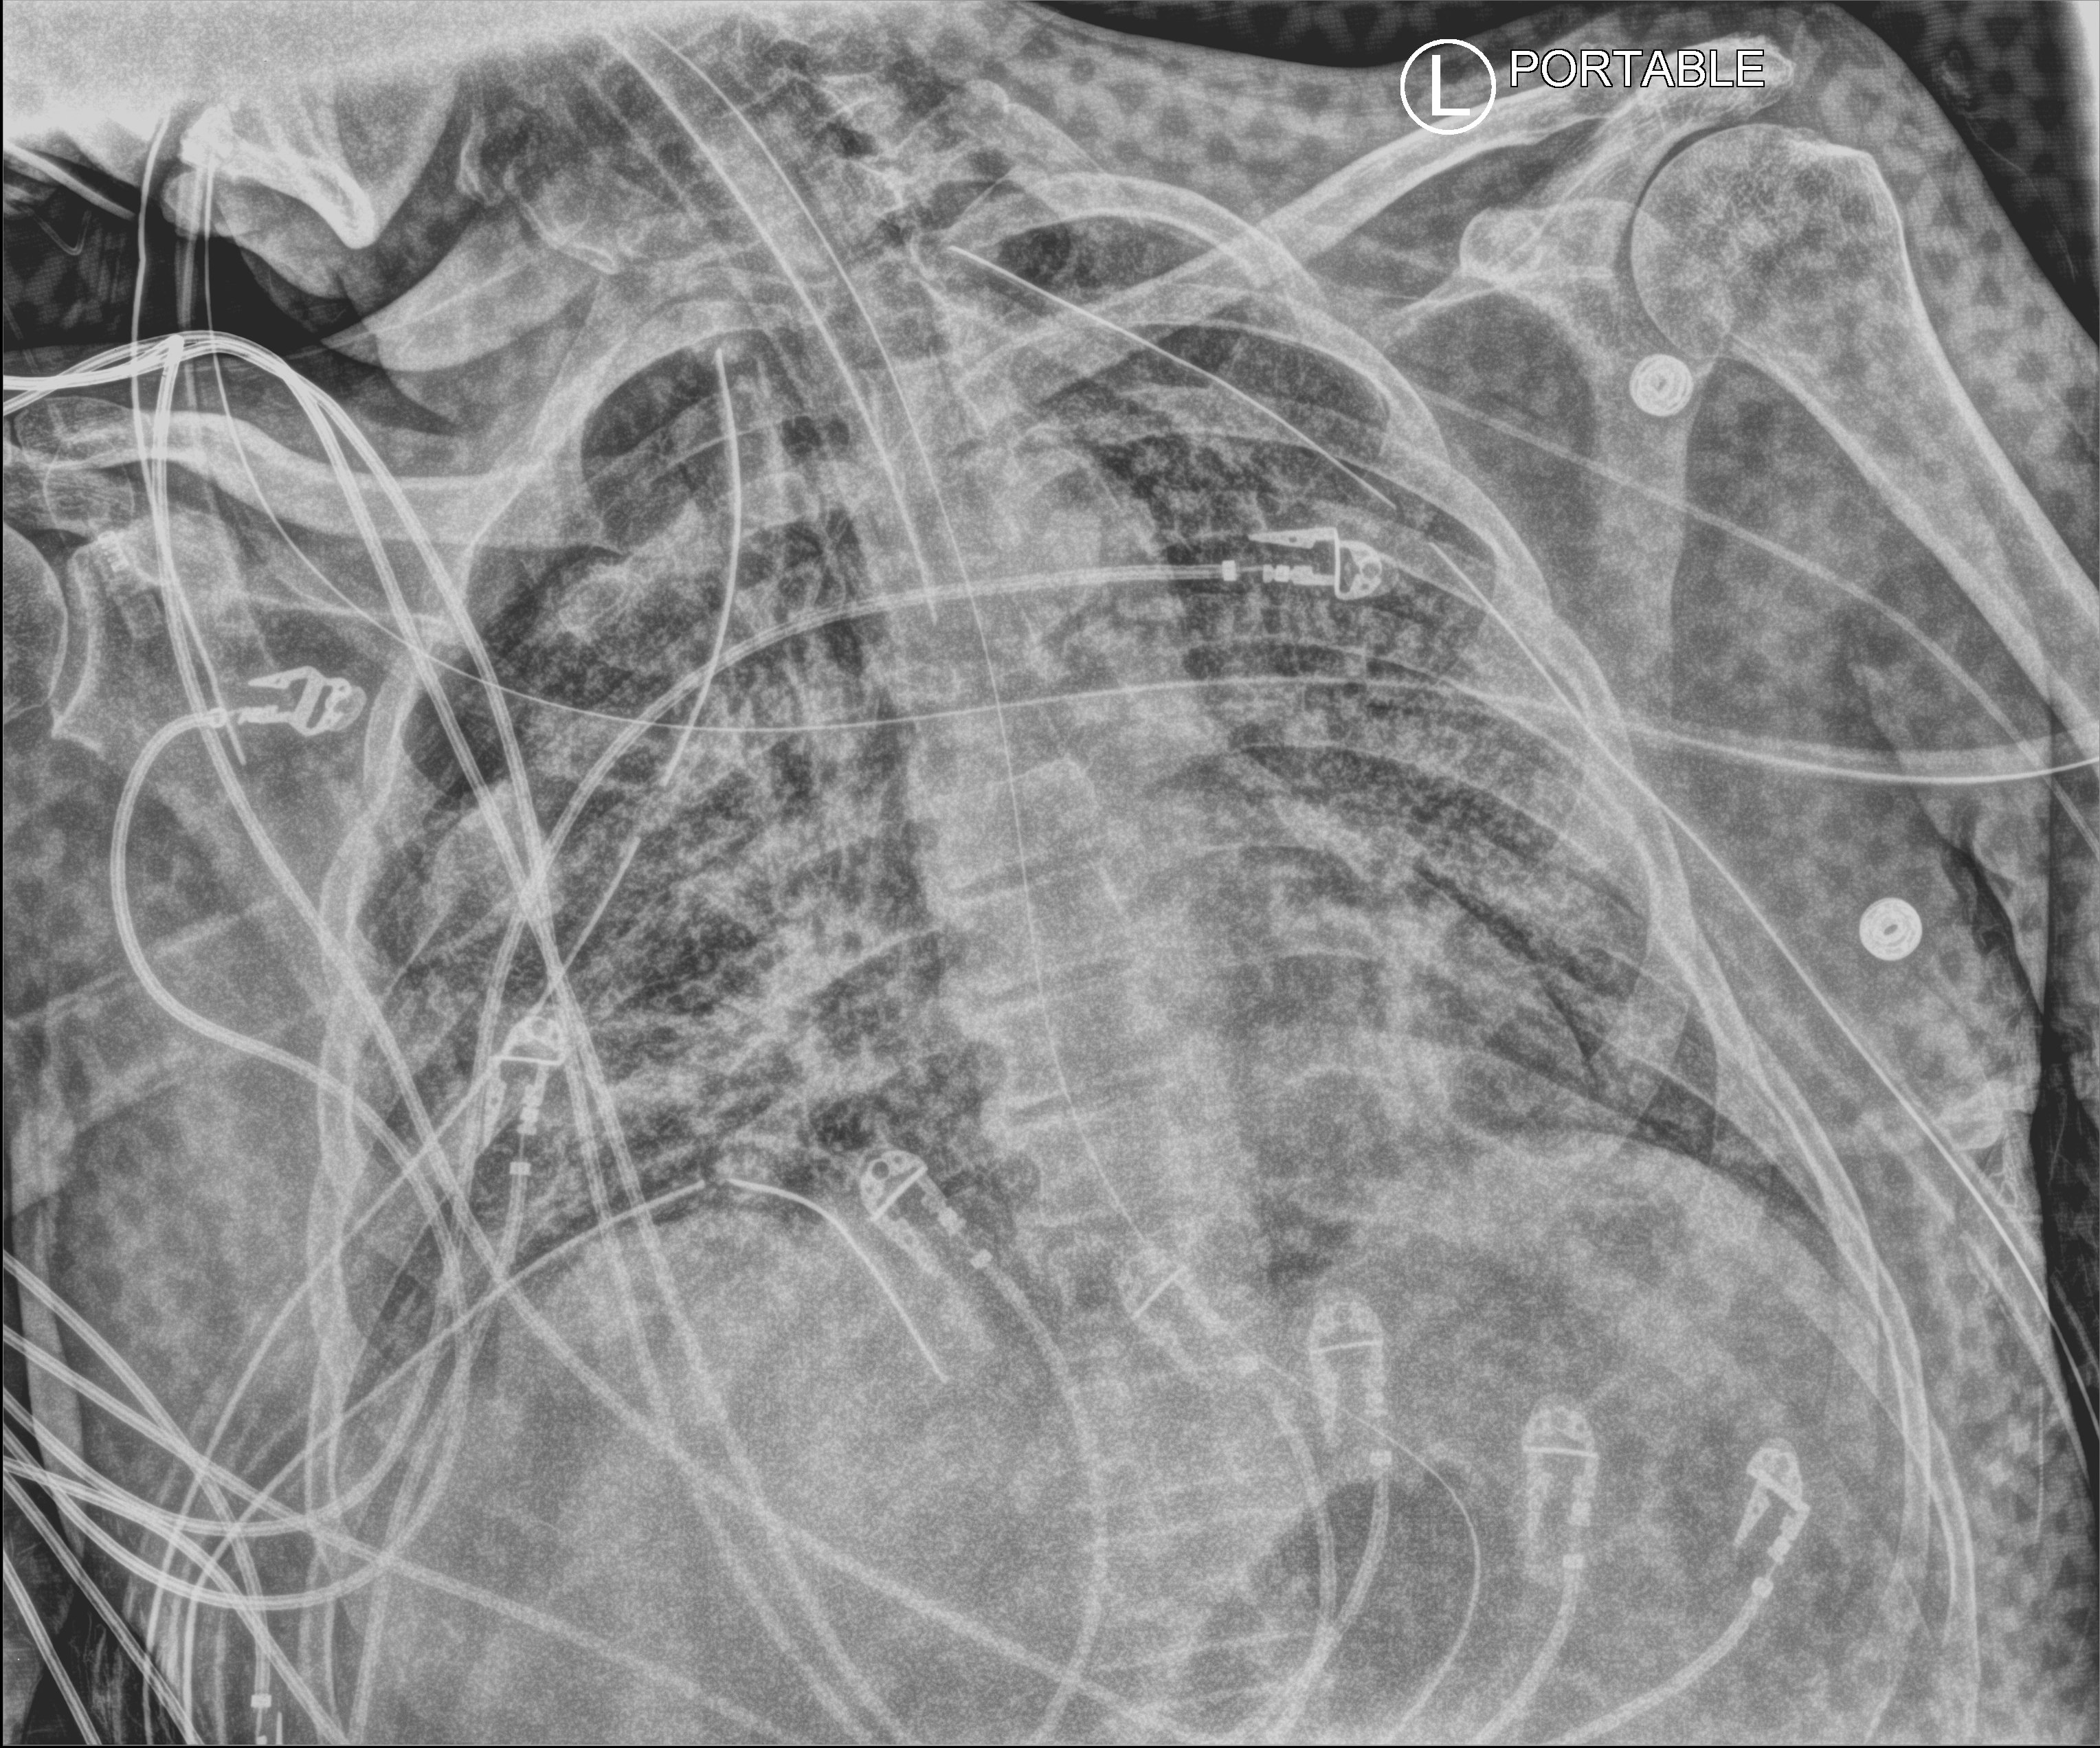
Chest X-ray (portable); anteroposterior (AP) projection. Male patient hospitalised with COVID-19, age 18–59 years.
Hospital-stay facts (about this admission, not read from this image; timing relative to this image not recorded):
- mechanically ventilated during this hospital stay: yes
- admitted to intensive care during this hospital stay: yes
- hypertension (admission record): yes